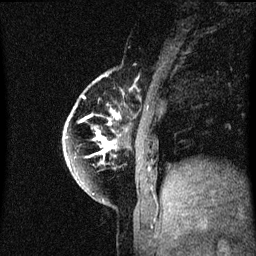
Breast MRI (dynamic contrast-enhanced), one sagittal slice. Slice 13 of 60 in the series (ordered by position). Dynamic contrast-enhanced series, image 2 of 3 at this slice position (ordered by acquisition). 1.5 T. TE 4.2 ms, TR 8.4 ms. 2 mm slice thickness. 256 × 256 image matrix. Female patient, age 60 years.
Outlined on this slice (semi-automatically segmented with operator editing):
- analysis volume of interest (the breast-tissue region the enhancement analysis was run in; not a lesion): bounding box [x1, y1, x2, y2] px = [64, 74, 127, 195]
- tumour enhancement mask (voxels above the 70 % enhancement threshold inside the analysis volume of interest): [64, 76, 119, 195]